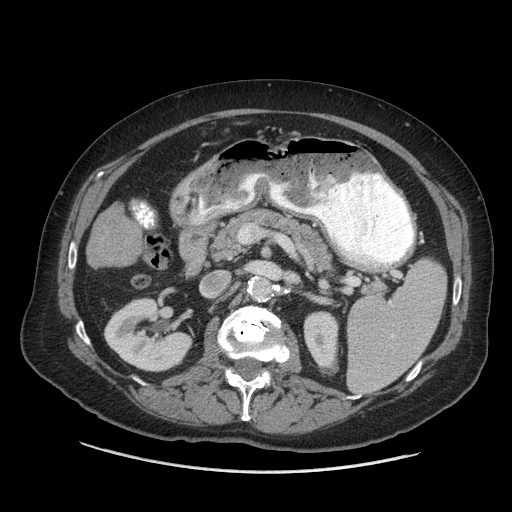
Contrast-enhanced abdominal CT (liver protocol), one axial slice. Slice 22 of 77 in the series (ordered by position). Reconstruction kernel STANDARD. 140 kVp. Soft-tissue window (W 400 / L 40 HU). 2.5 mm slice thickness. 512 × 512 image matrix, field of view 420 × 420 mm. From the clinical record (not read from this slice): diagnosis: hepatocellular carcinoma (patient treated with transarterial chemoembolisation; whether this scan precedes or follows treatment is not stated here); TNM stage (as recorded): Stage-I; Child-Pugh class: A; tumour differentiation: well differentiated; tumour nodularity: uninodular.
Outlined on this slice (semi-automatic segmentation, software-assisted and operator-edited):
- liver parenchyma outside the tumour (the mass and vessels are separate outlines, so this box may not span the whole liver): bounding box (x1, y1, x2, y2) in pixels: (92, 206, 139, 246)